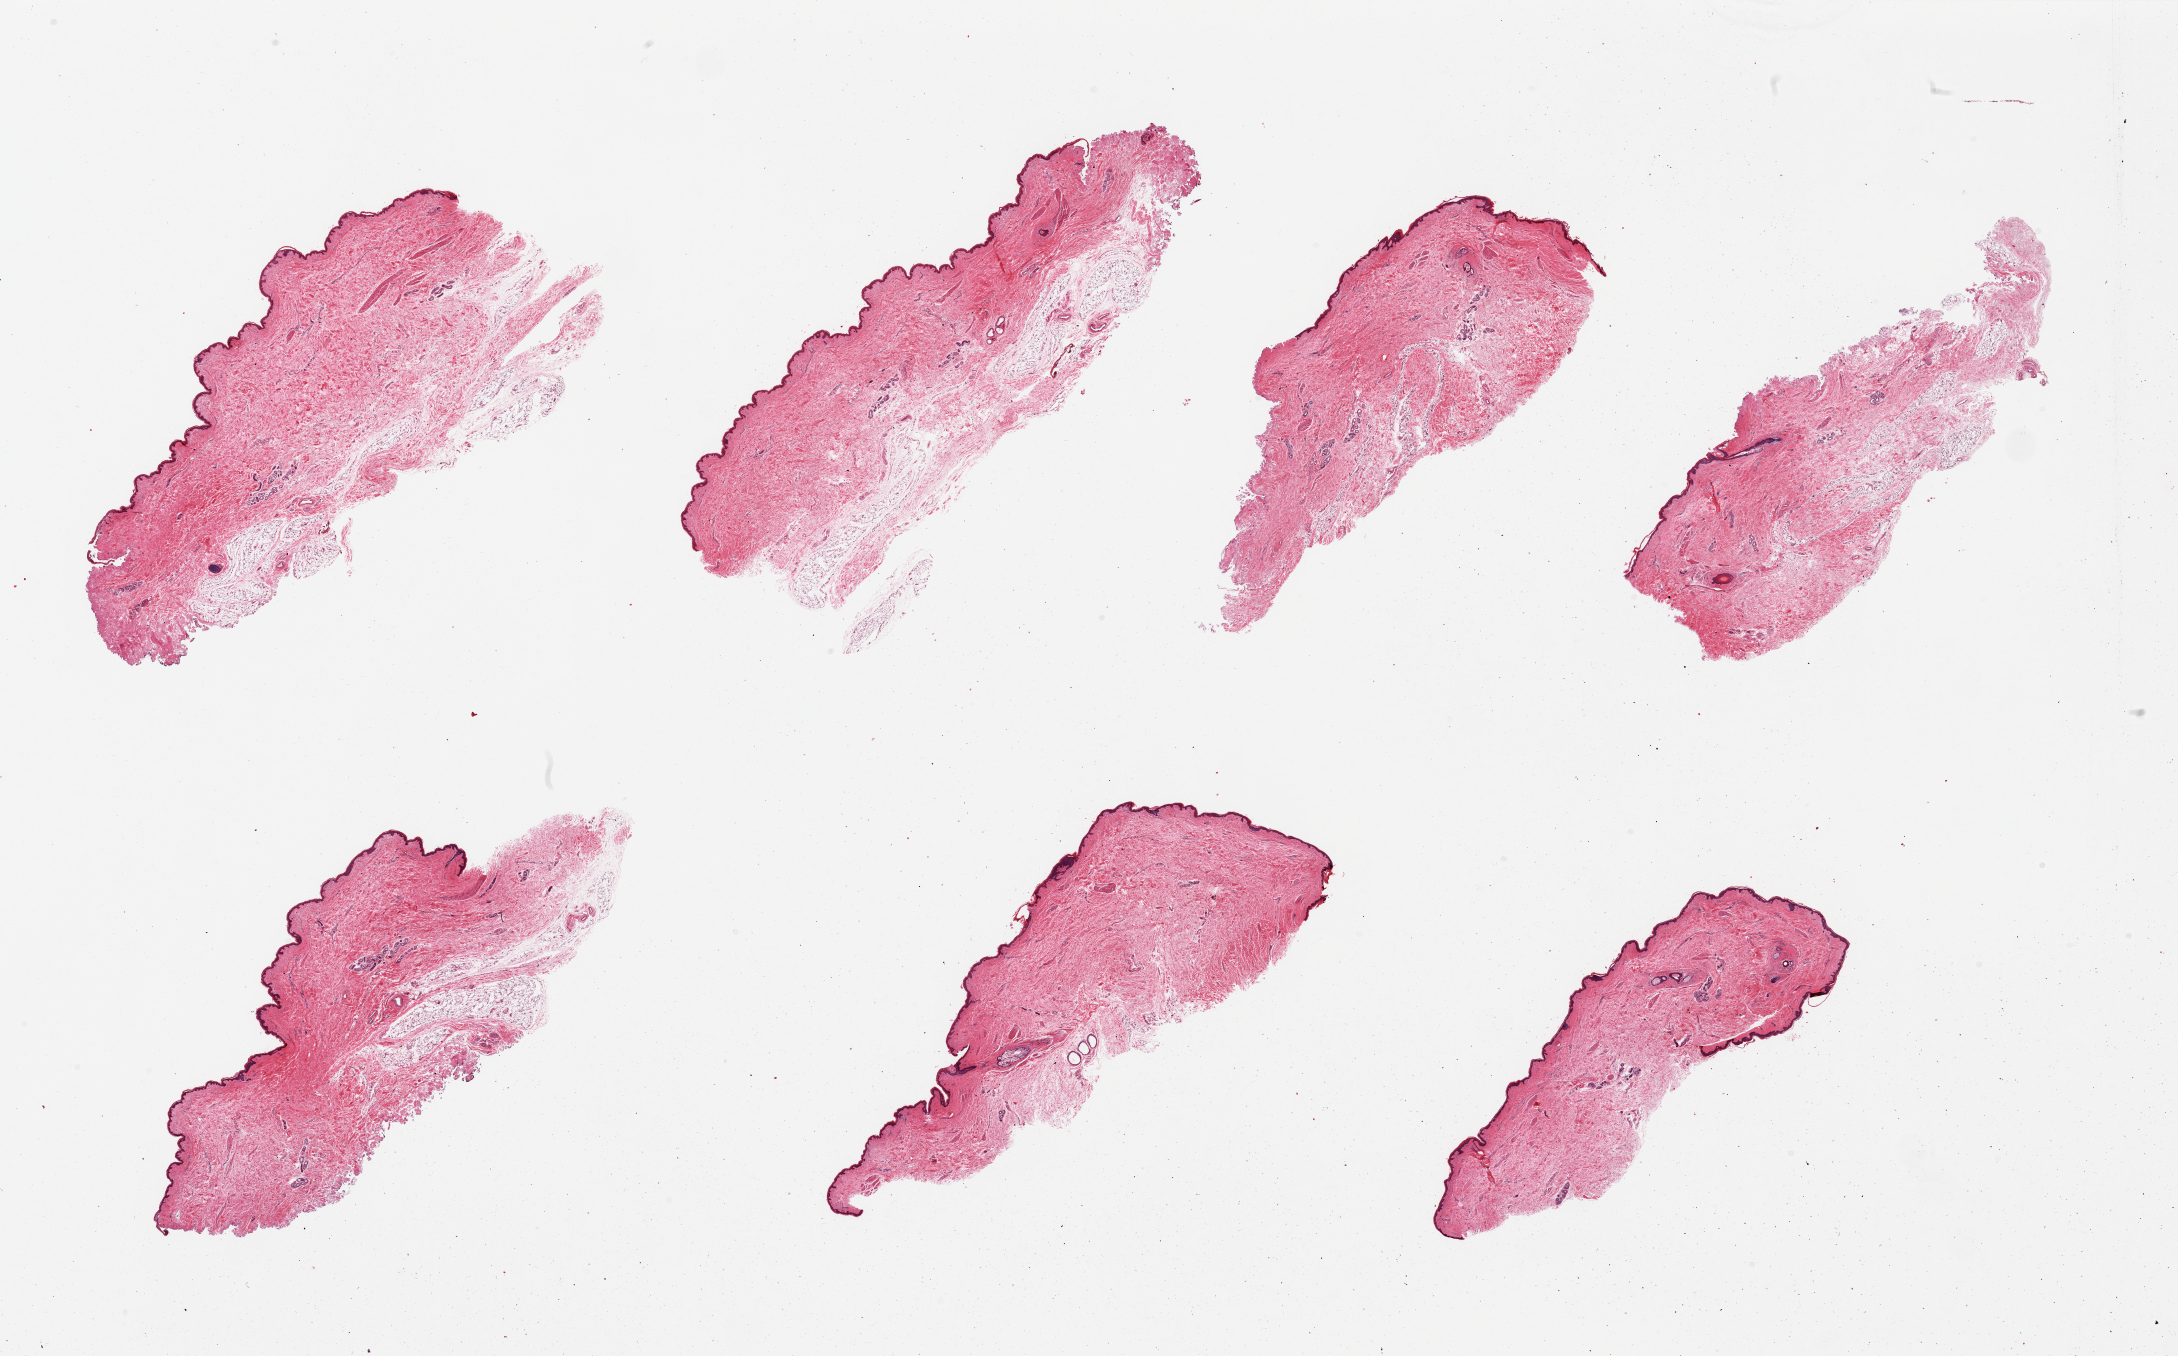
Digitized haematoxylin and eosin-stained section, whole scanned area (about 34.5 x 21.5 mm) shown as a low-resolution overview; PAXgene-fixed, paraffin-embedded tissue; section of skin of suprapubic region (target tissue); tissue donor sample.
Pathologist's review note for this sample: 7 pieces; no obvious fibrosis or vasculitis; 10% dermal fat.